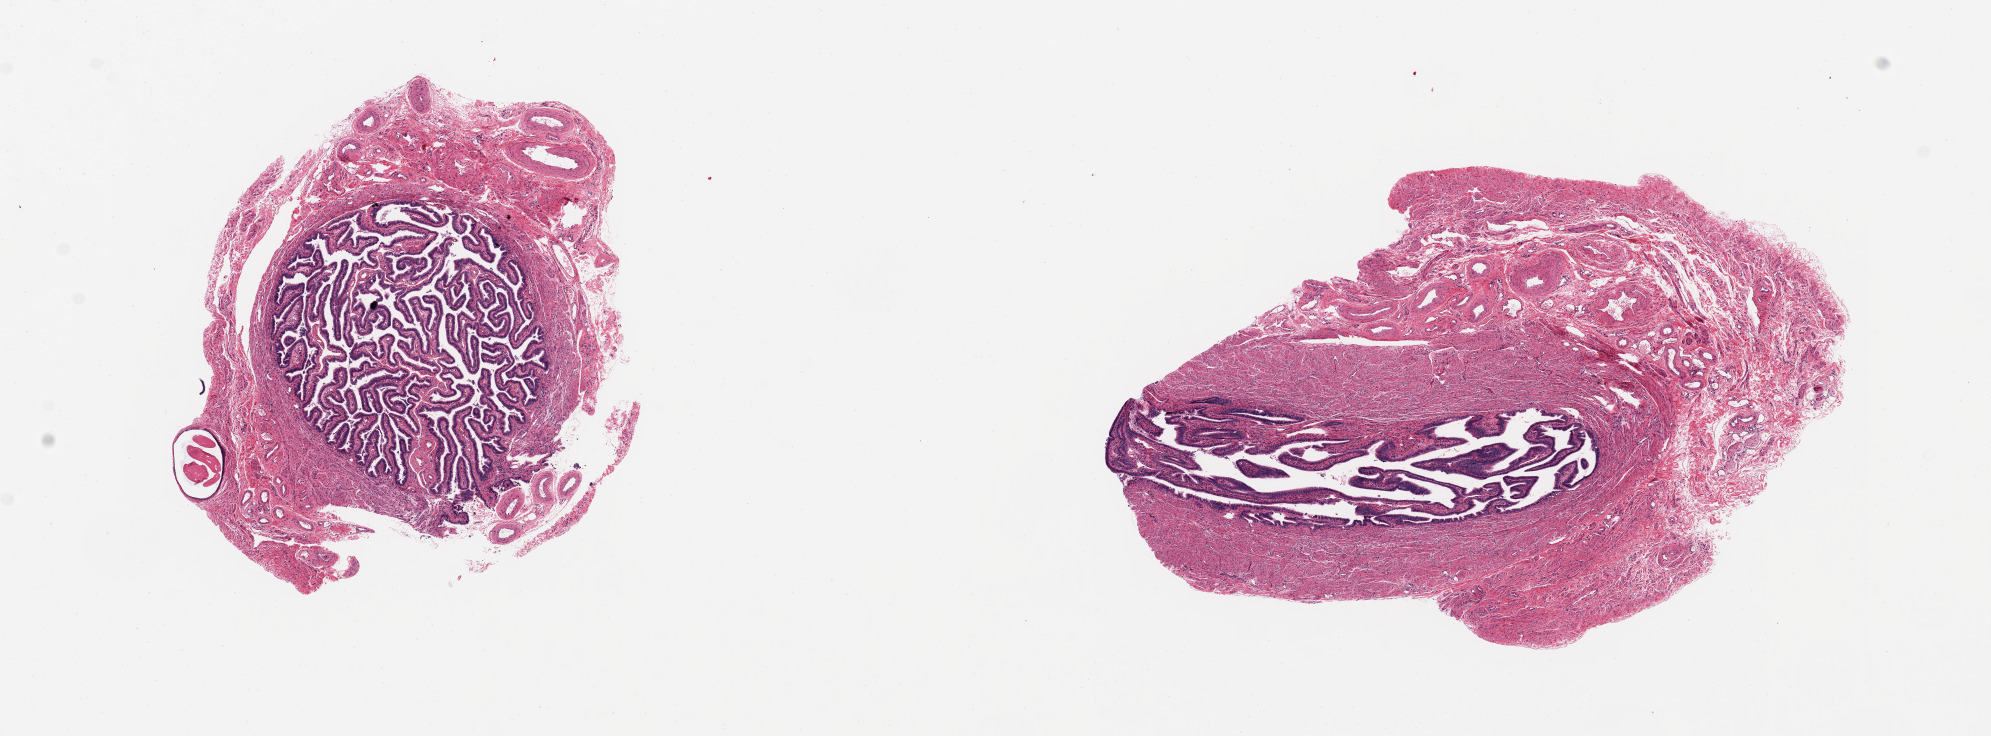
Hematoxylin and eosin (H&E) whole-slide image, brightfield, whole scanned area (about 15.8 x 5.8 mm, from a 20x scan) shown as a low-resolution overview. PAXgene-fixed paraffin-embedded (PFPE) section. Section of fallopian tube (target tissue). Donor tissue sample. Donor: female.
- review note (as recorded): 2 pieces up to 5x3 mm; good epithelium